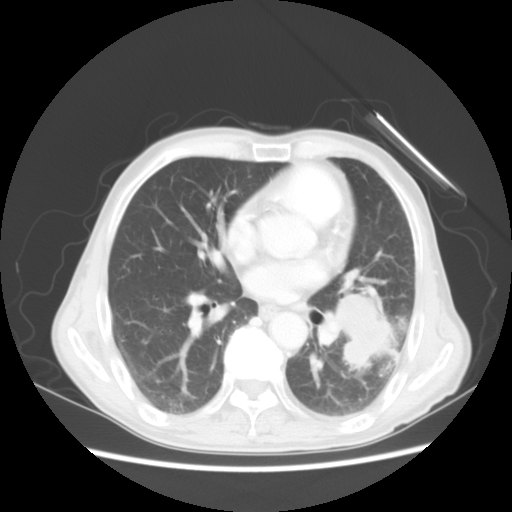
Chest CT, one axial slice. Position 24 of 51 along the scan axis. Reconstruction kernel STANDARD. 120 kVp. Lung window (W 1500 / L -600 HU). 512 × 512 image matrix. Patient: male, 64 years. Case-level facts recorded for this patient, not image findings: clinical TNM (as recorded): T4 N0 M0; histopathological grade: G2-3.
Outlined on this slice (bounding box drawn by a radiologist):
- lung tumour (recorded histology: squamous cell carcinoma): bounding box <321,273,400,381> (left, top, right, bottom; pixels)